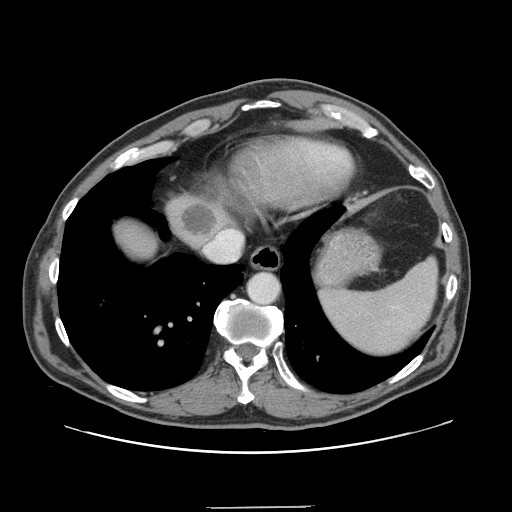
Contrast-enhanced abdominal CT, one axial slice; position 129 of 139 along the scan axis; 120 kVp; intravenous contrast given; soft-tissue window (W 400 / L 40 HU); 512 × 512 image matrix, field of view 397 × 397 mm. Male patient, age 64 years. Case-level facts recorded for this patient, not image findings: diagnosis: colorectal cancer liver metastases, imaged before liver resection; multiple liver metastases: yes; largest metastasis: 3.5 cm; chemotherapy before resection: yes.
Outlined on this slice (outlined manually by an expert reader):
- liver: bounding box (x1, y1, x2, y2) in pixels: (119, 195, 229, 255)
- planned liver remnant (the part of the liver to remain after resection): (118, 225, 156, 256)
- liver metastasis: (183, 206, 216, 236)